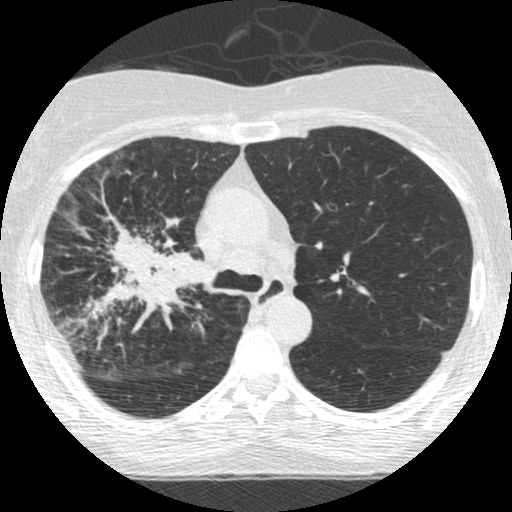
Low-dose screening chest CT, one axial slice; reconstruction kernel STANDARD; 120 kVp; lung window (W 1500 / L -600 HU); 1.25 mm slice thickness; 512 × 512 image matrix, field of view 294 × 294 mm.
Outlined on this slice (outlined manually by an expert reader):
- lesion 2 (tumor, hilum of right lung): bounding box [x1, y1, x2, y2] px = [91, 215, 209, 314]